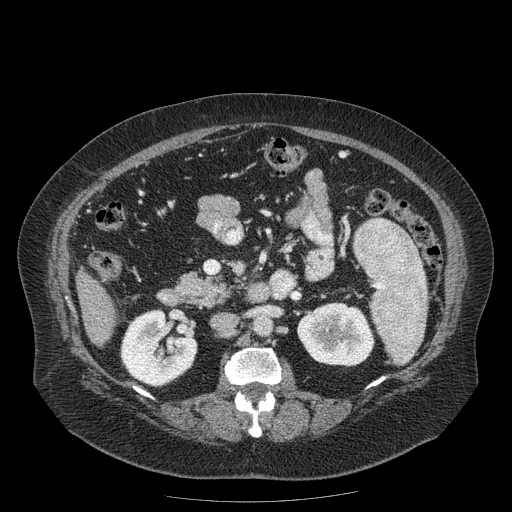
Contrast-enhanced abdominal CT (liver protocol), one axial slice; slice 57 of 204 in the series (ordered by position); 120 kVp; soft-tissue window (W 400 / L 40 HU); 2.5 mm slice thickness; 512 × 512 image matrix, field of view 440 × 440 mm. From the clinical record (not read from this slice): diagnosis: hepatocellular carcinoma (patient treated with transarterial chemoembolisation; whether this scan precedes or follows treatment is not stated here); TNM stage (as recorded): Stage-IIIB; Child-Pugh class: A; tumour differentiation: well differentiated.
Structures marked on this image (semi-automatic segmentation, software-assisted and operator-edited):
- liver parenchyma outside the tumour (the mass and vessels are separate outlines, so this box may not span the whole liver): bounding box (x1, y1, x2, y2) in pixels: (76, 268, 116, 345)